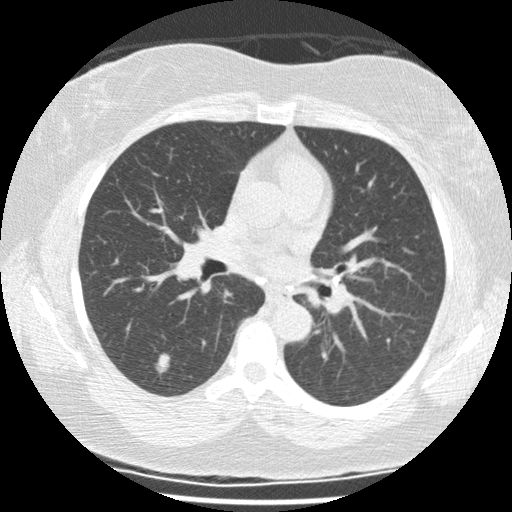
Low-dose screening chest CT, axial slice, second screening round (one year after baseline), lung window (W 1500 / L -600 HU), standard (soft-tissue) reconstruction kernel (STANDARD), slice 54 of 117 in the series, 512 × 512 image matrix, field of view 325 × 325 mm. Female, age 65 years at enrolment. Current smoker at enrolment.
Lesion marked by an expert reader, box from (x=140, y=346) to (x=181, y=385) px. The exam's reader record, not a measurement of the box and not confirmed to be the same lesion: non-calcified nodule or mass ≥4 mm, right lower lobe, 12 × 8 mm, spiculated (stellate) margins, mixed attenuation, pre-existing on the prior screen: yes; interval growth: yes.